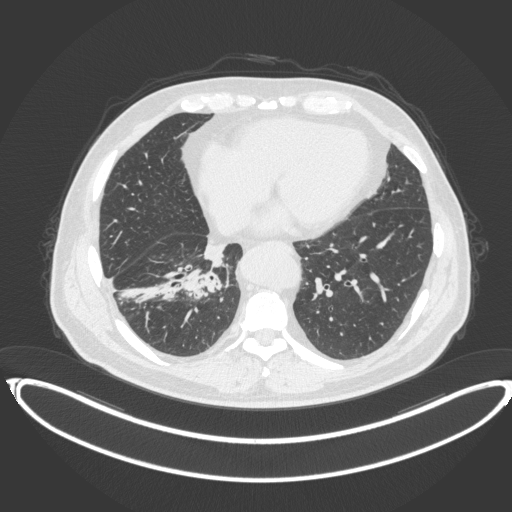
Chest CT, one axial slice. Position 144 of 383 along the scan axis. Reconstruction kernel B31f. Lung window (W 1500 / L -600 HU). 1 mm slice thickness. 512 × 512 image matrix, field of view 448 × 448 mm. Patient: male, 61 years. Case-level facts recorded for this patient, not image findings: clinical TNM (as recorded): T1b N1 M0.
Structures marked on this image (rectangle marked by the reading radiologist):
- lung tumour (recorded histology: squamous cell carcinoma): bounding box <182,260,226,305> (left, top, right, bottom; pixels)